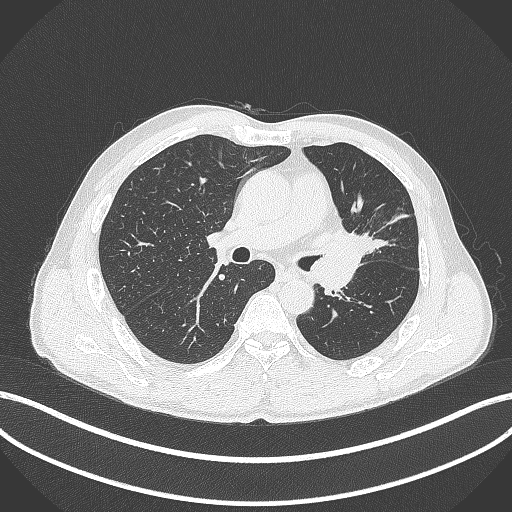
Chest CT, one axial slice; position 246 of 429 along the scan axis; reconstruction kernel B70f; lung window (W 1500 / L -600 HU); 512 × 512 image matrix. Male patient, age 57 years. Case-level facts recorded for this patient, not image findings: clinical TNM (as recorded): T2b N0 M0.
Annotated regions visible in this slice (rectangle marked by the reading radiologist):
- lung tumour (recorded histology: squamous cell carcinoma): bounding box (x1, y1, x2, y2) in pixels: (323, 223, 374, 261)